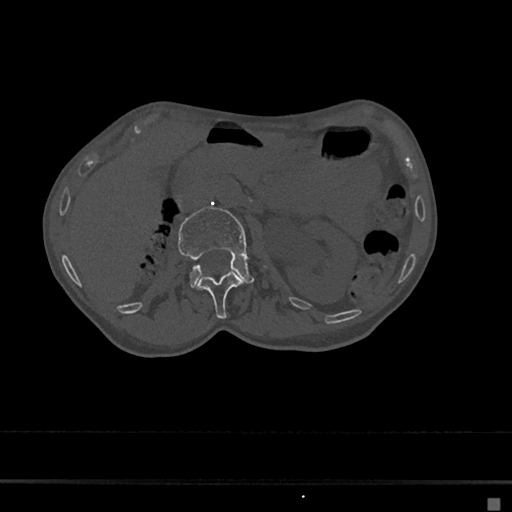
CT including the spine, one axial slice. Position 42 of 797 along the scan axis. Reconstruction kernel Br40s/3. 120 kVp. Bone window (W 1800 / L 400 HU). 0.5 mm slice thickness. 512 × 512 image matrix. Patient: female, 68 years. From the clinical record (not read from this slice): primary cancer: renal.
Outlined on this slice (semi-automatically segmented with operator editing):
- L1 vertebra: bounding box (x1, y1, x2, y2) in pixels: (197, 272, 241, 319)
- L2 vertebra: (178, 207, 253, 287)